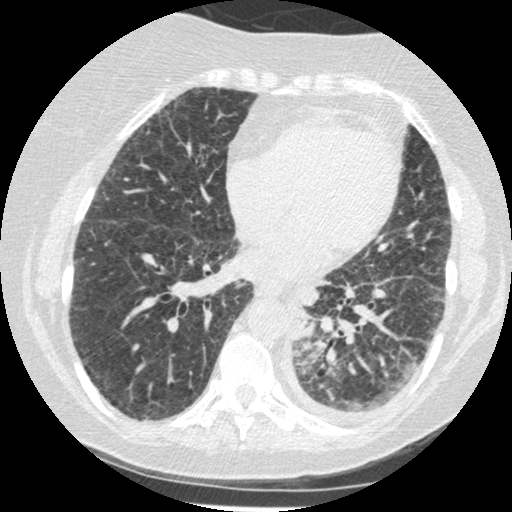
Low-dose screening chest CT, one axial slice. Position 78 of 341 along the scan axis. Reconstruction kernel STANDARD. 120 kVp. Lung window (W 1500 / L -600 HU). 1.25 mm slice thickness. 512 × 512 image matrix.
Structures marked on this image (expert manual segmentation):
- lesion 1 (tumor, lower lobe of left lung): bounding box <294,323,314,339> (left, top, right, bottom; pixels)